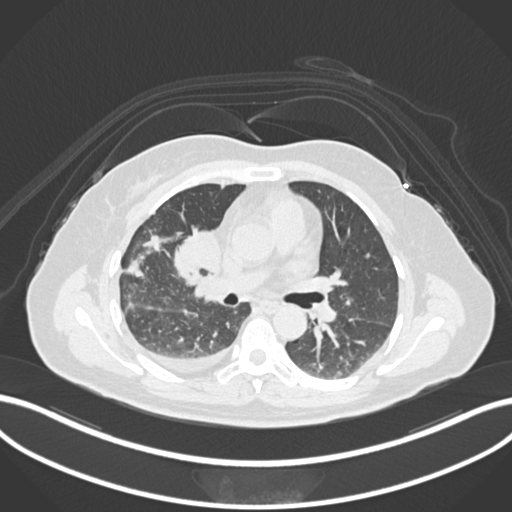
Chest CT, one axial slice. Slice 78 of 172 in the series (ordered by position). Reconstruction kernel B30f. 120 kVp. Lung window (W 1500 / L -600 HU). 512 × 512 image matrix. Female patient, age 52 years. From the clinical record (not read from this slice): clinical TNM (as recorded): T3 N1 M1.
Outlined on this slice (bounding box drawn by a radiologist):
- lung tumour (recorded histology: adenocarcinoma): bounding box (x1, y1, x2, y2) in pixels: (174, 224, 224, 280)